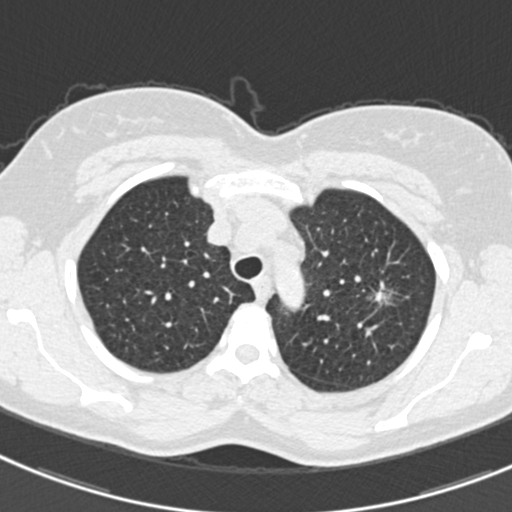
Low-dose screening chest CT, one axial slice. Slice 249 of 309 in the series (ordered by position). Lung window (W 1500 / L -600 HU). 1 mm slice thickness. 512 × 512 image matrix.
Annotated regions visible in this slice (outlined manually by an expert reader):
- lesion 1 (tumor, upper lobe of left lung): bounding box <375,292,389,304> (left, top, right, bottom; pixels)